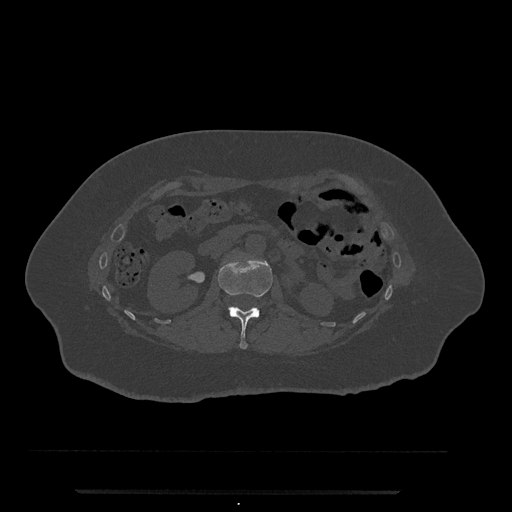
CT including the spine, one axial slice; slice 91 of 797 in the series (ordered by position); reconstruction kernel Br40s/3; 120 kVp; bone window (W 1800 / L 400 HU); 0.5 mm slice thickness; 512 × 512 image matrix, field of view 440 × 440 mm. Female patient, age 51 years. Case-level facts recorded for this patient, not image findings: primary cancer: neuro.
Annotated regions visible in this slice (semi-automatic segmentation, software-assisted and operator-edited):
- L1 vertebra: bounding box <218,256,273,349> (left, top, right, bottom; pixels)
- L2 vertebra: <228,306,233,309>